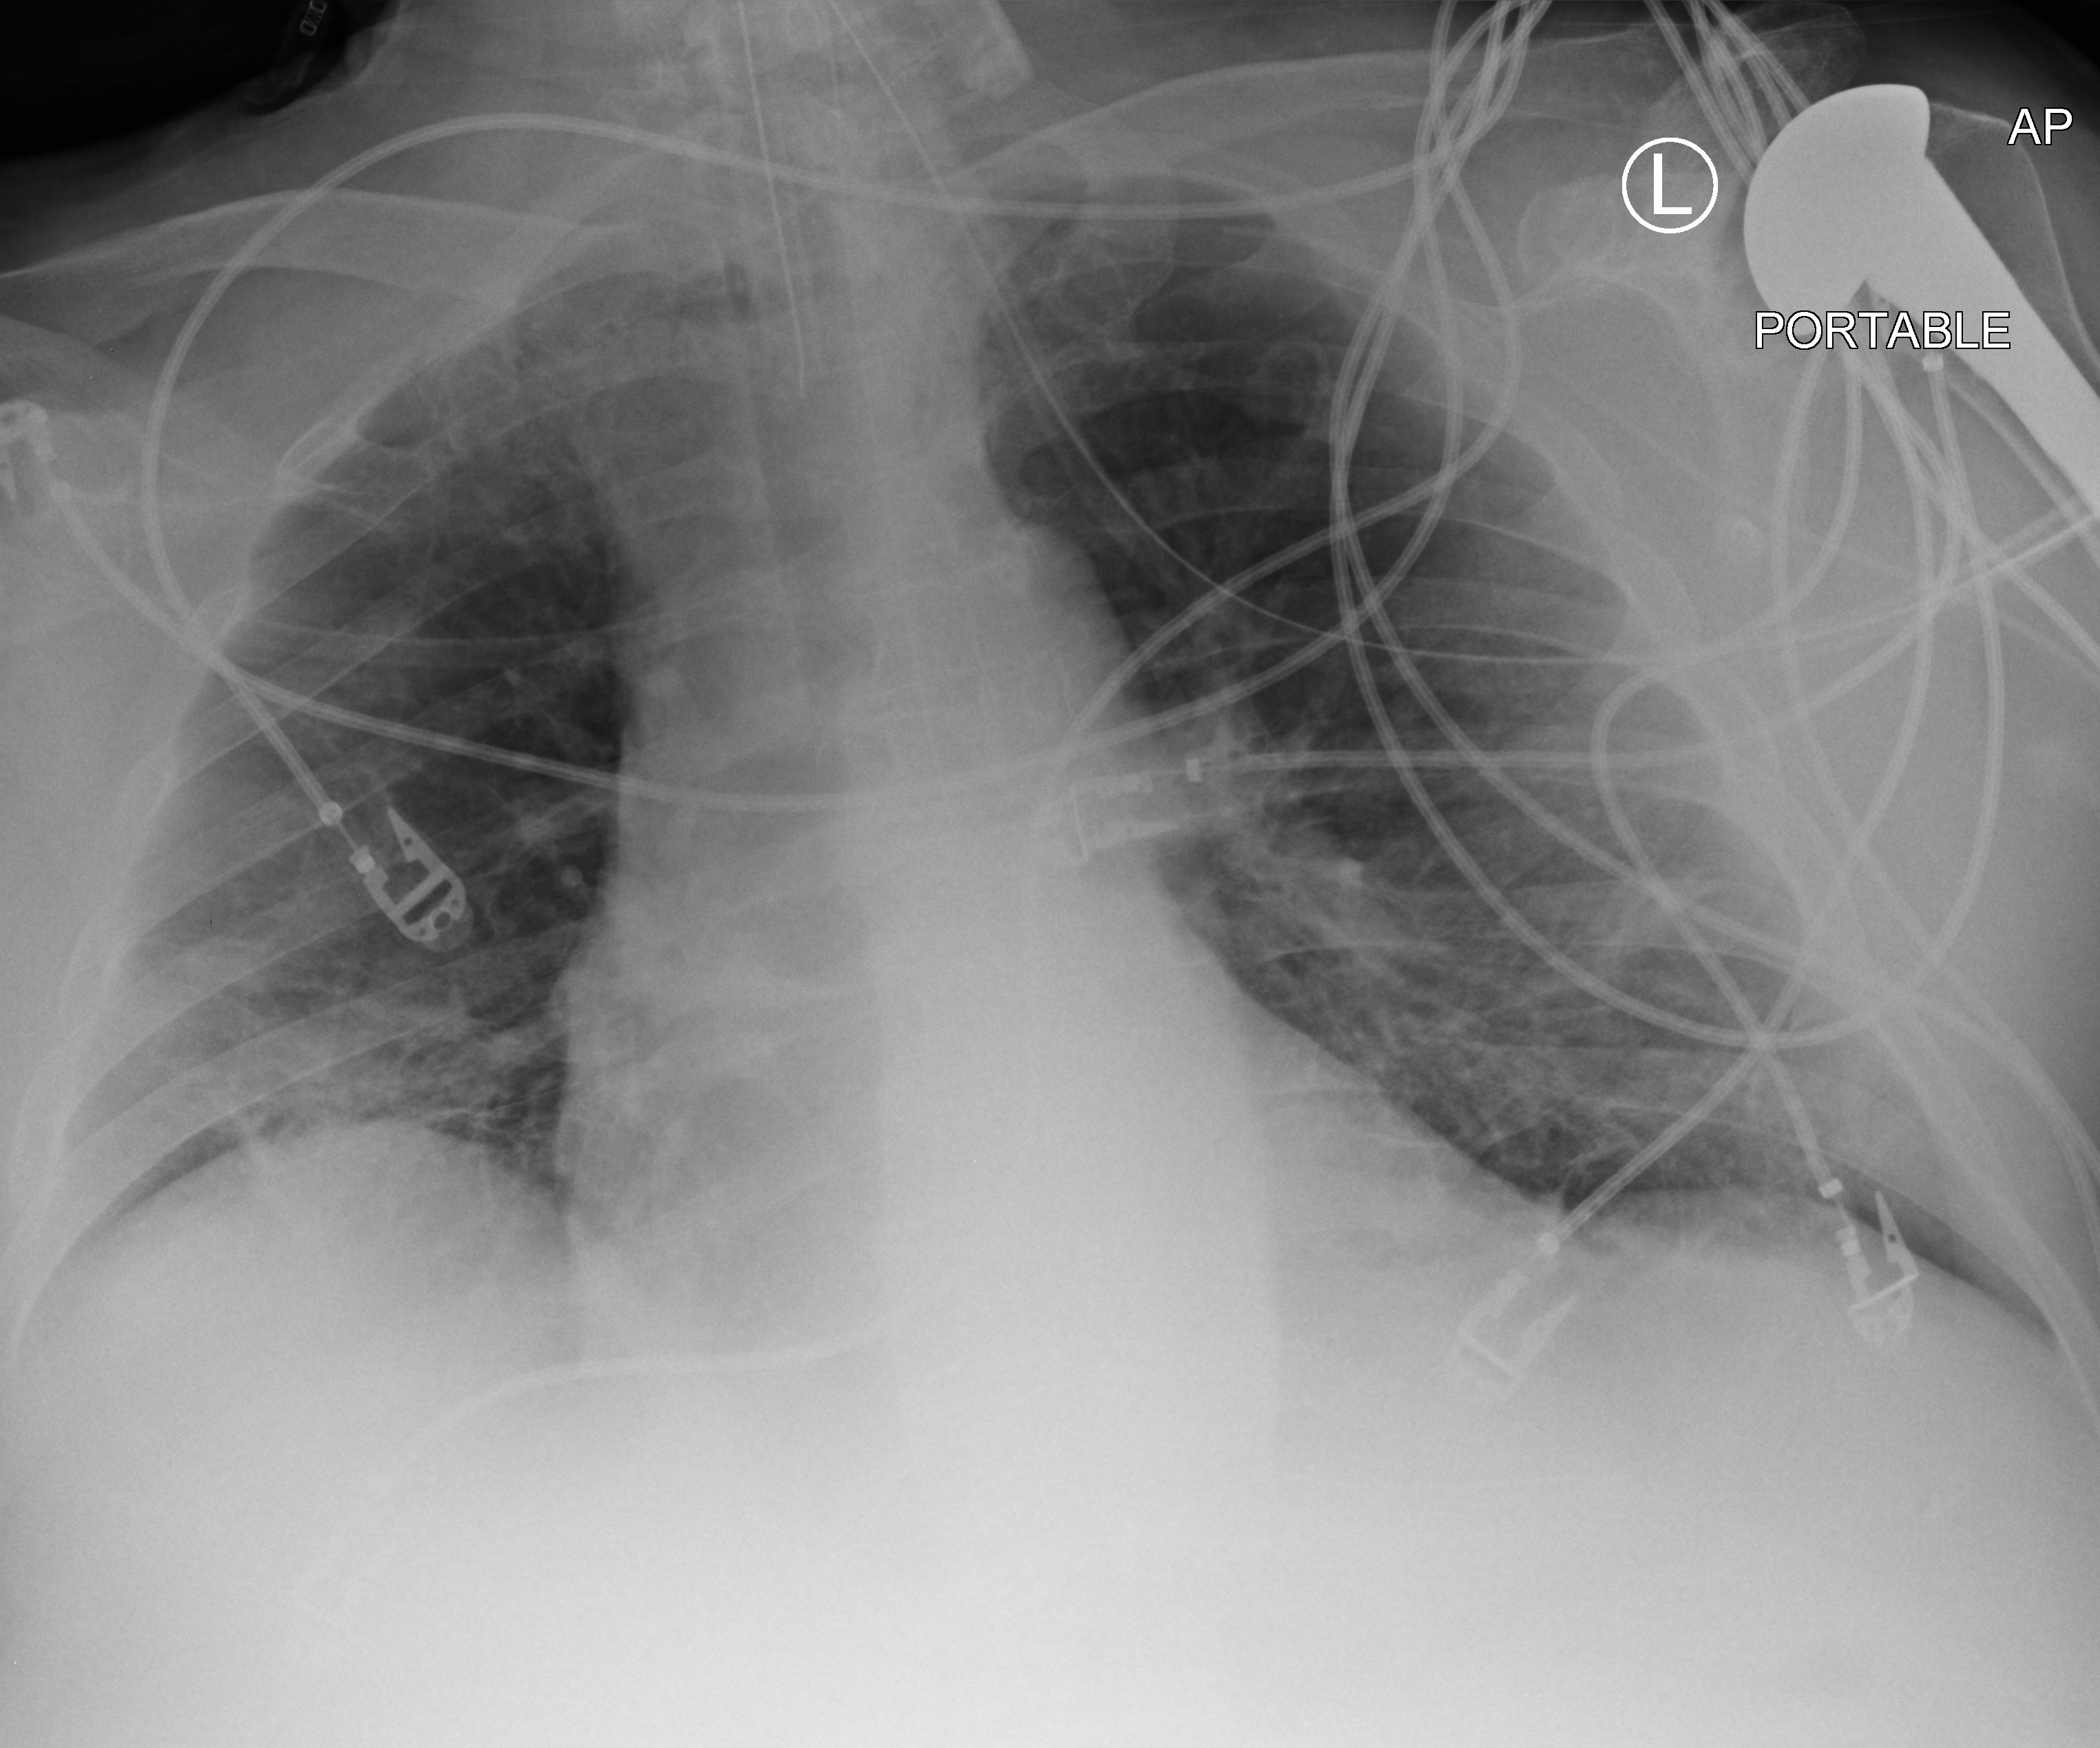
Chest X-ray (portable); anteroposterior (AP) projection. Patient hospitalised with COVID-19; male, aged 60–74 years.
Admission-level facts for this patient (not findings on this image; timing relative to this image not recorded): mechanically ventilated during this hospital stay: yes; other chronic lung disease (admission record): no.